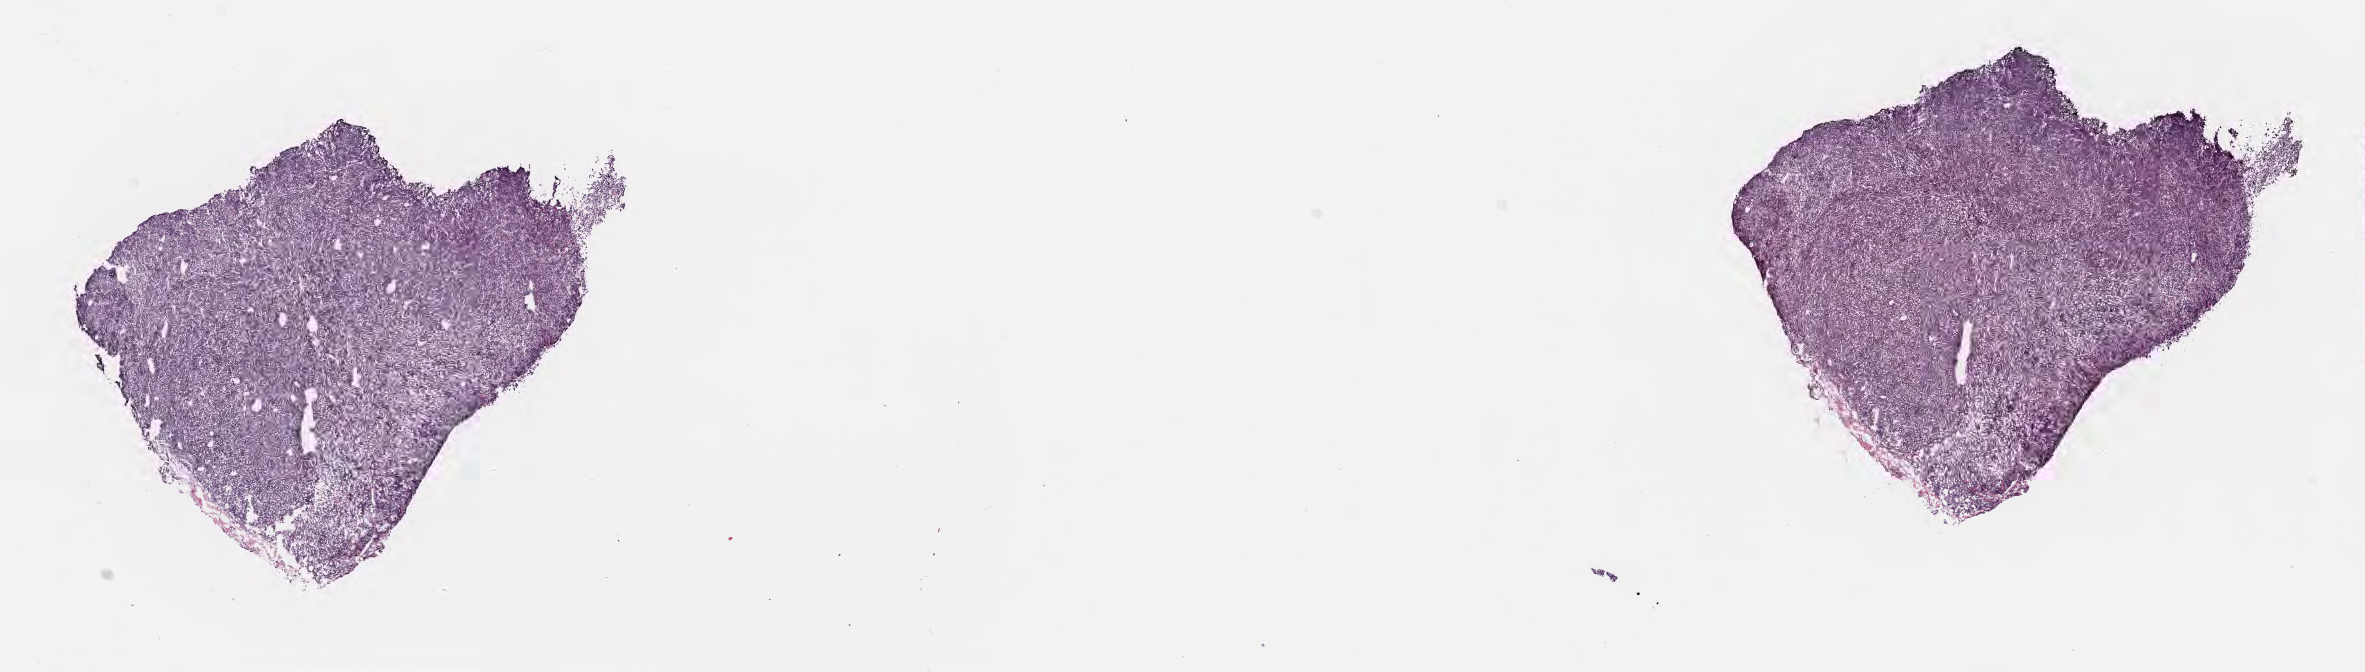
Whole-slide image, haematoxylin and eosin stain — a low-resolution overview of the entire scanned area, about 19.1 x 5.4 mm; frozen section (tissue freezing medium); specimen: primary tumor; anatomic site: cranium. Male, age 6 years at initial diagnosis. Composition of this section per pathologist review: tumor cells 95%, tumor nuclei 95%, stromal cells 5%, necrosis 0%, normal cells 0%. Inflammatory infiltration, as recorded: lymphocyte infiltration 40%, monocyte infiltration 35%, neutrophil infiltration 5%.
* diagnosis: Diffuse large B-cell lymphoma, NOS
* Ann Arbor stage (patient): Stage I